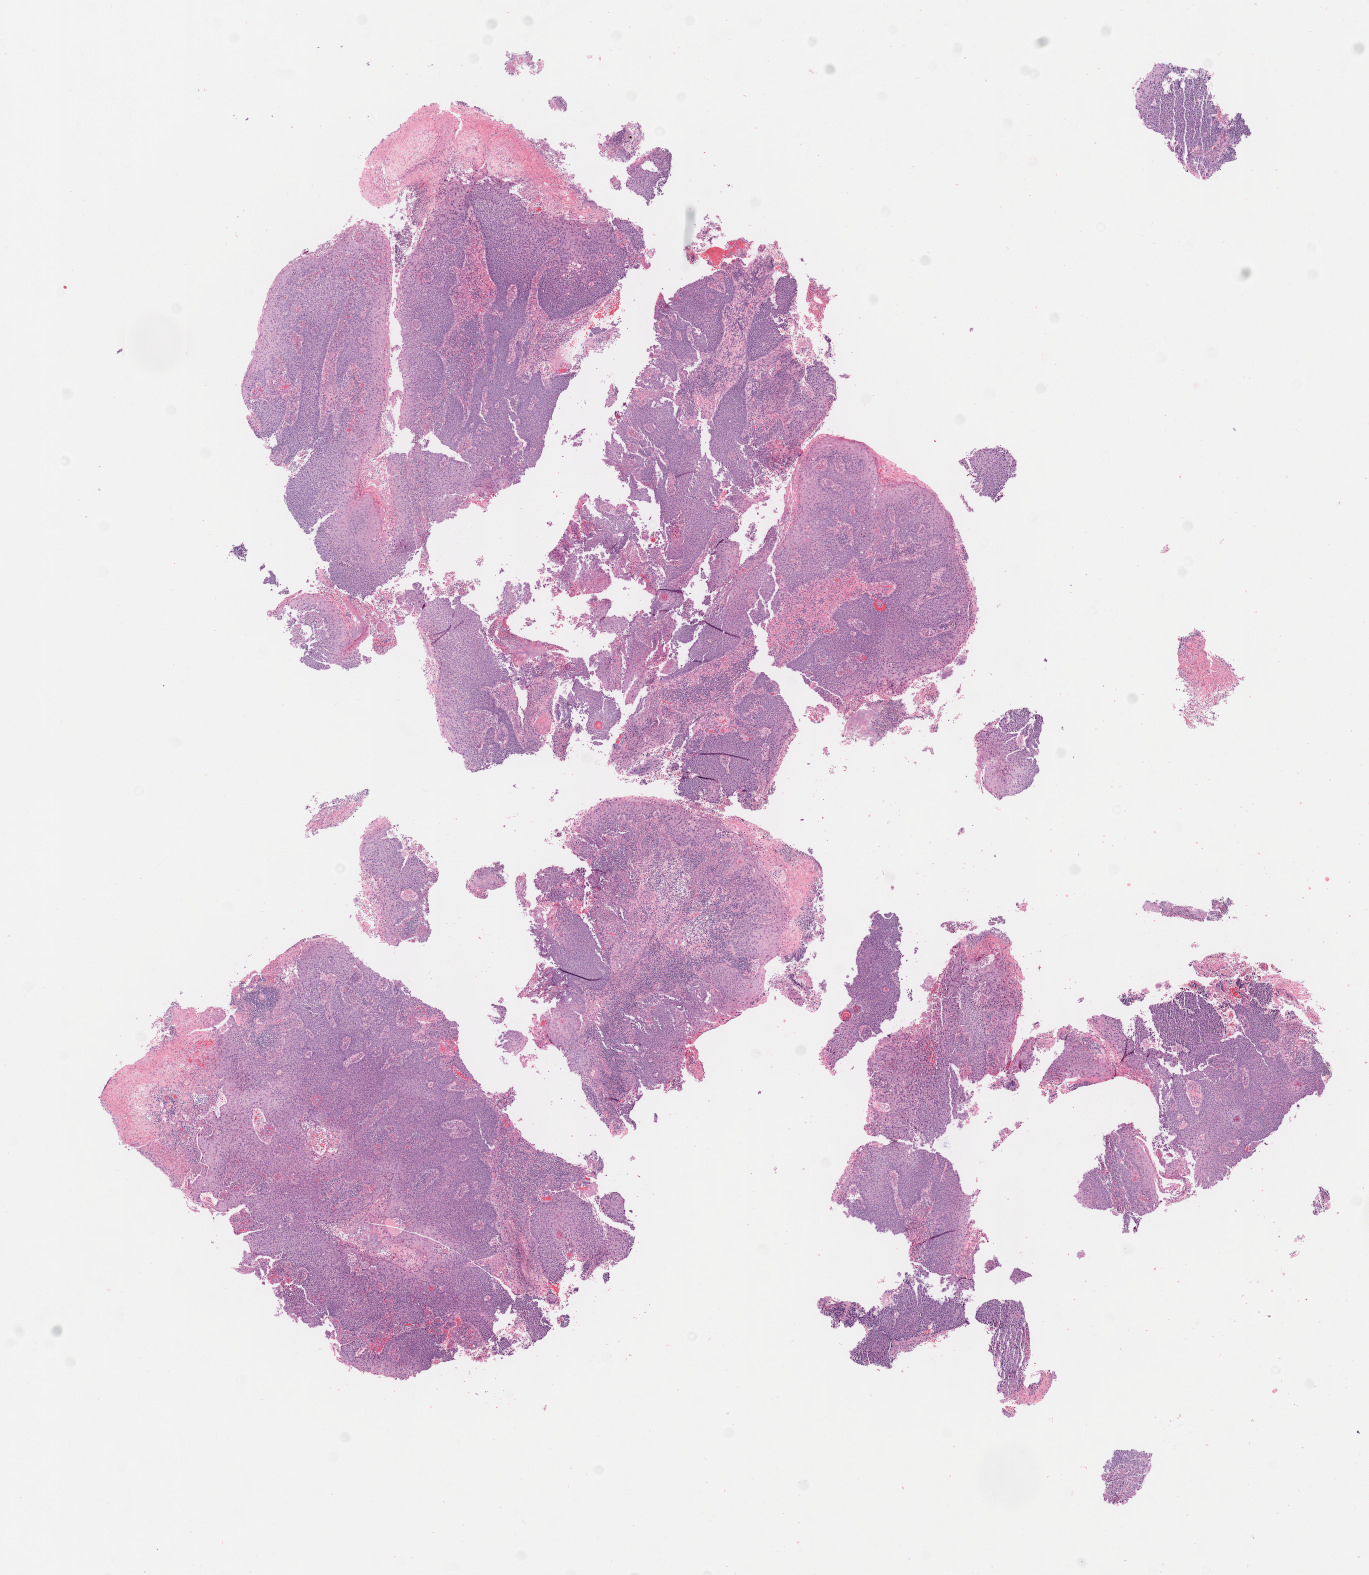
Whole-slide image, hematoxylin and eosin (H&E) stain — a low-resolution overview of the entire scanned area, about 11.1 x 12.7 mm, specimen: tumor tissue, site: cervix. Patient female; 45 years old.
Diagnosis: Squamous cell carcinoma, large cell, nonkeratinizing, NOS.